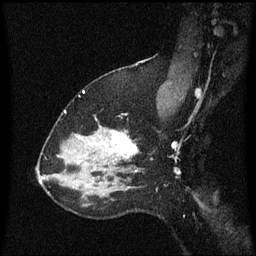
Breast MRI (dynamic contrast-enhanced), one sagittal slice. Position 44 of 60 along the scan axis. Dynamic contrast-enhanced series, image 2 of 3 at this slice position (ordered by acquisition). 1.5 T. TE 4.2 ms, TR 8.4 ms. 2 mm slice thickness. 256 × 256 image matrix, field of view 200 × 200 mm. Patient: female, 37 years. From the clinical record (not read from this slice): setting: breast cancer imaged before/during neoadjuvant chemotherapy; receptor status: HR-positive, HER2-negative.
Outlined on this slice (semi-automatic segmentation, software-assisted and operator-edited):
- analysis volume of interest (the breast-tissue region the enhancement analysis was run in; not a lesion): bounding box (x1, y1, x2, y2) in pixels: (95, 114, 154, 171)
- tumour enhancement mask (voxels above the 70 % enhancement threshold inside the analysis volume of interest): (115, 132, 138, 157)